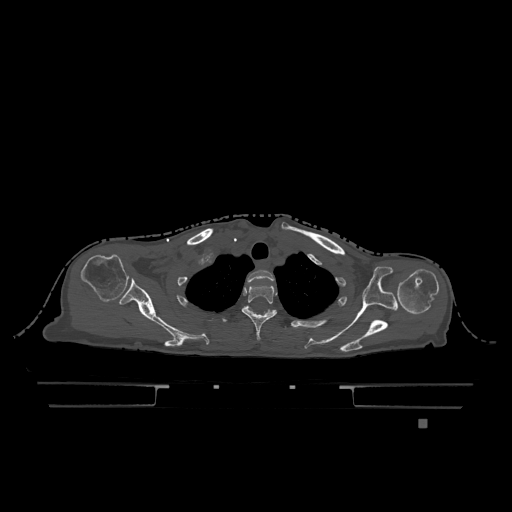
CT including the spine, one axial slice; position 959 of 1317 along the scan axis; bone window (W 1800 / L 400 HU); 0.5 mm slice thickness; 512 × 512 image matrix, field of view 500 × 500 mm. Female patient, age 74 years. From the clinical record (not read from this slice): primary cancer: lung; vertebrae with lytic lesions (as recorded): T1, T4, T5, T6, L4, L5.
Outlined on this slice (semi-automatic segmentation, software-assisted and operator-edited):
- T1 vertebra: bounding box [x1, y1, x2, y2] px = [247, 270, 274, 283]
- T2 vertebra: [241, 285, 277, 341]
- T3 vertebra: [246, 306, 272, 313]
- T6 vertebra: [248, 306, 274, 313]